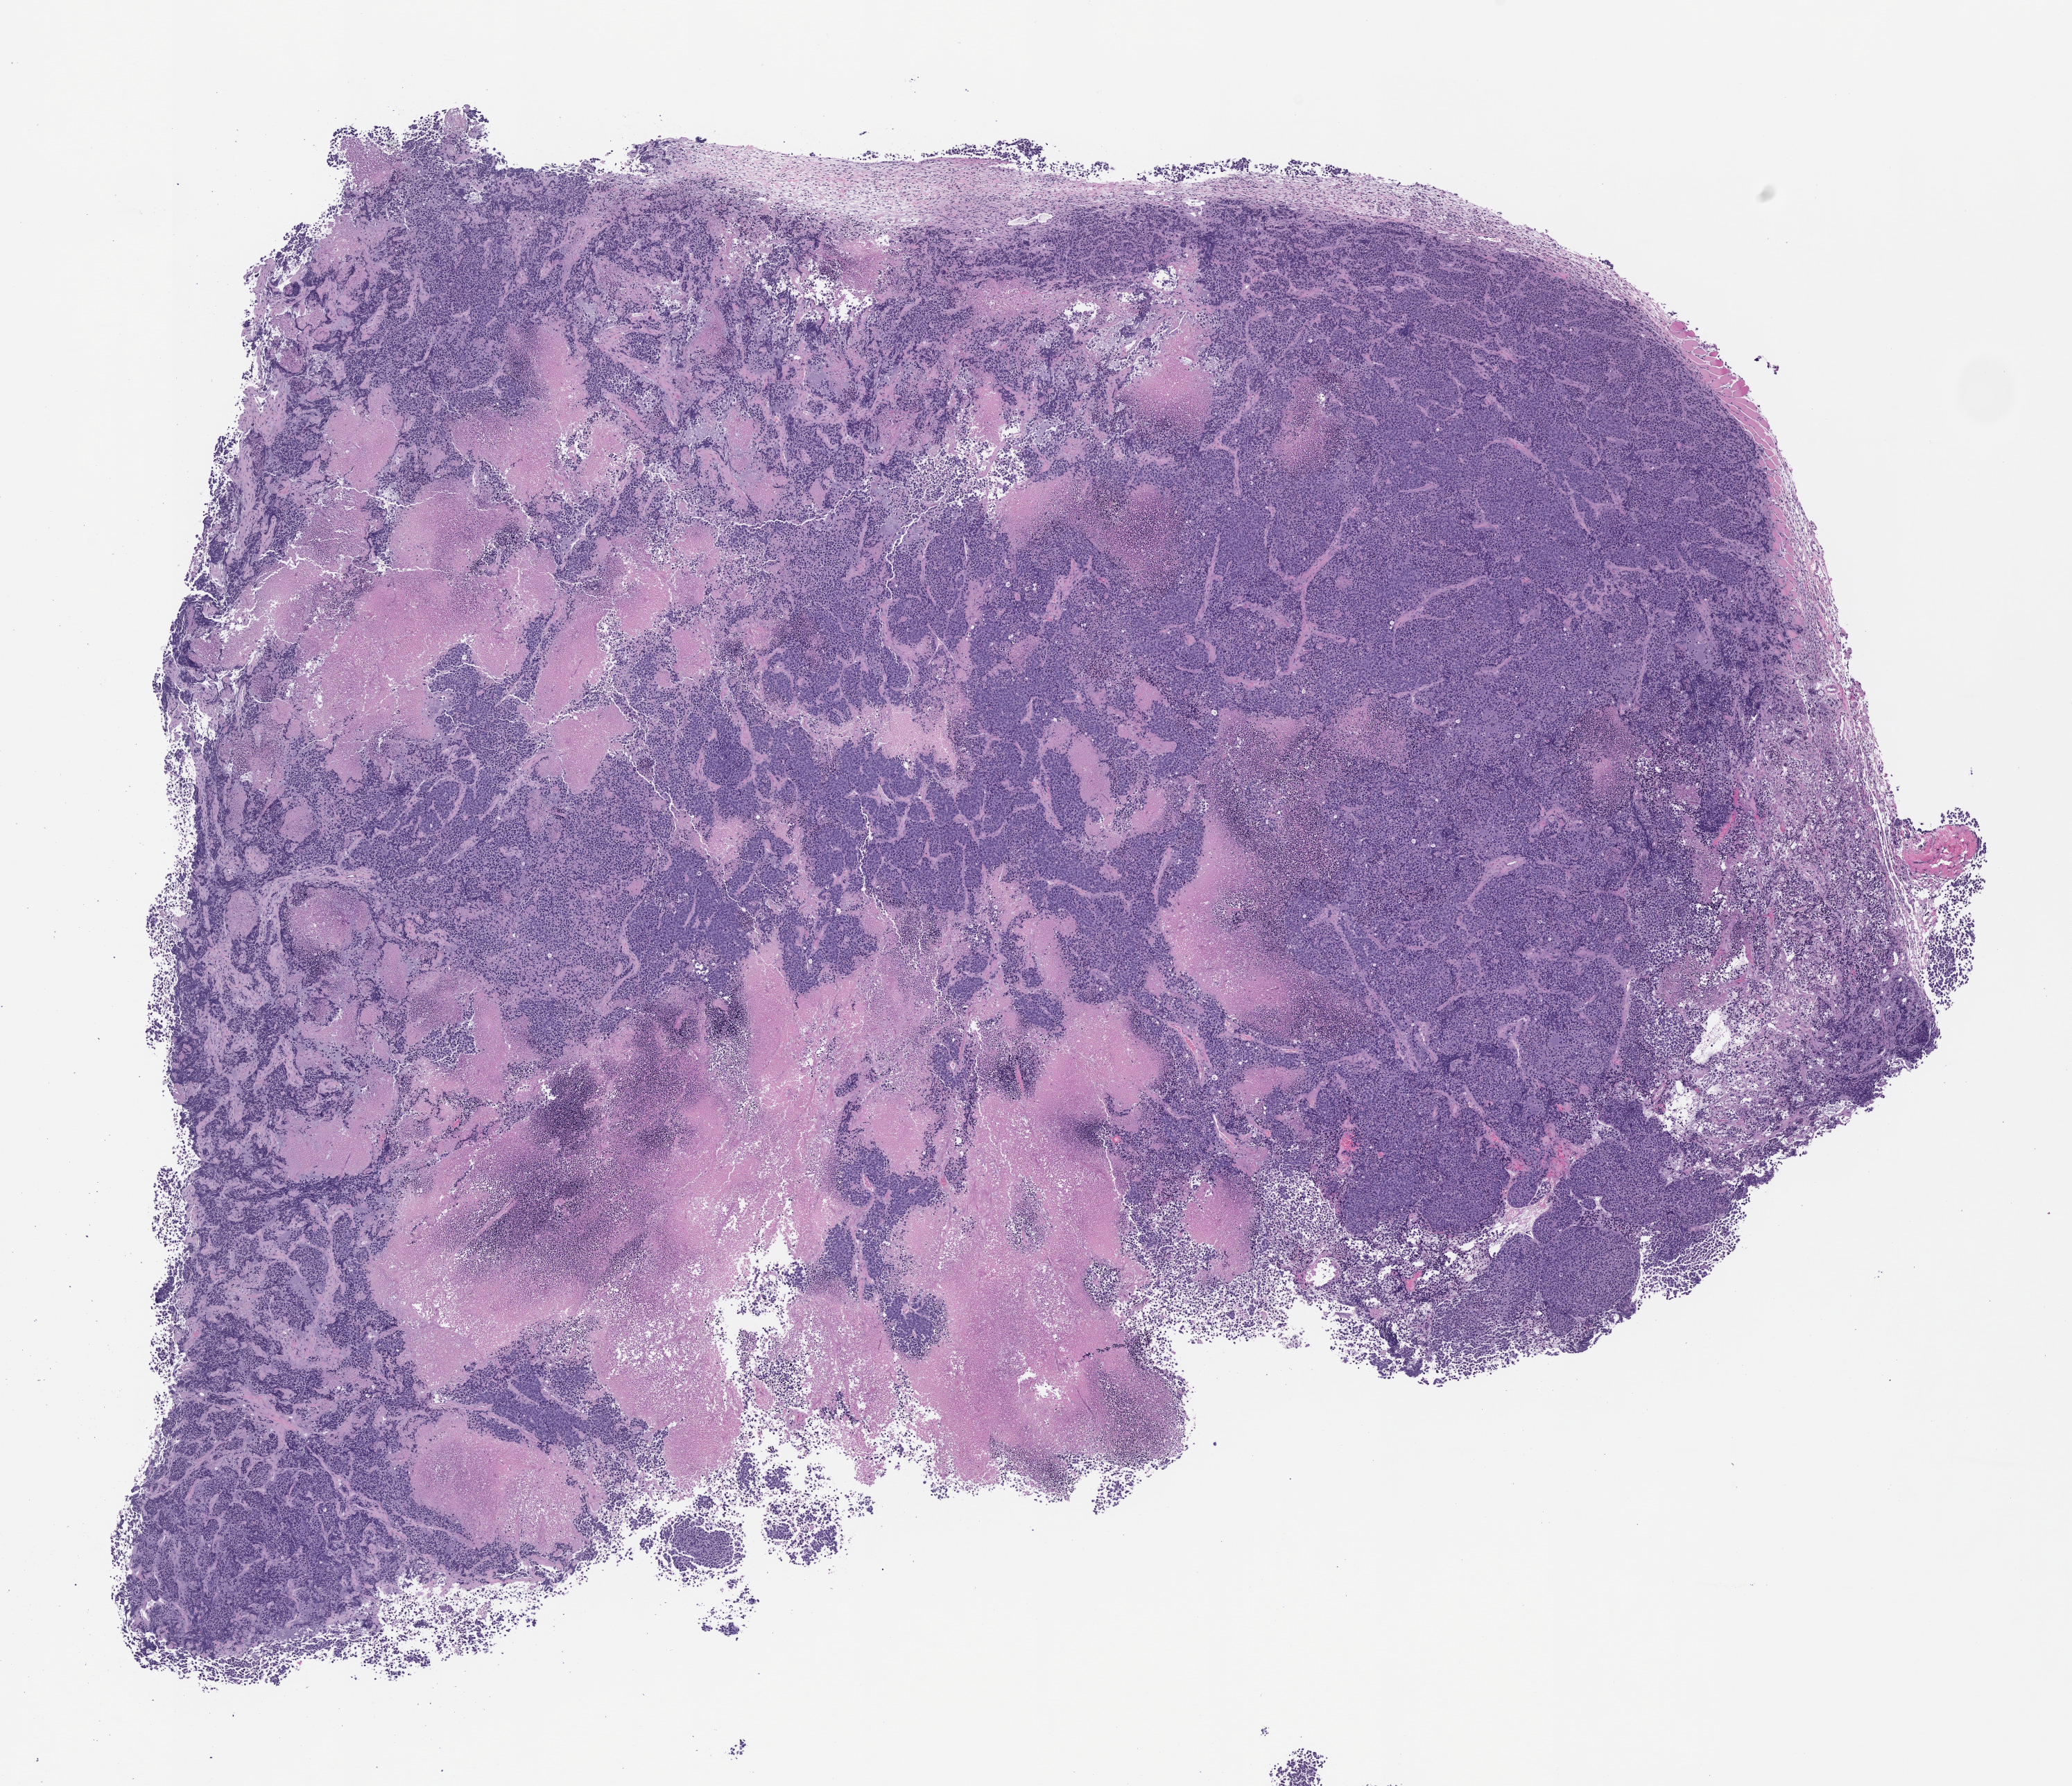
Hematoxylin and eosin (H&E) whole-slide image of a patient-derived xenograft (PDX) tumor grown in a mouse, passage 1 — shown as a low-resolution overview of the whole scanned area (about 12.0 x 10.4 mm); formalin-fixed paraffin-embedded section; tumor site category: neuroendocrine system.
Originating patient diagnosis: Neuroendocrine Carcinoma.